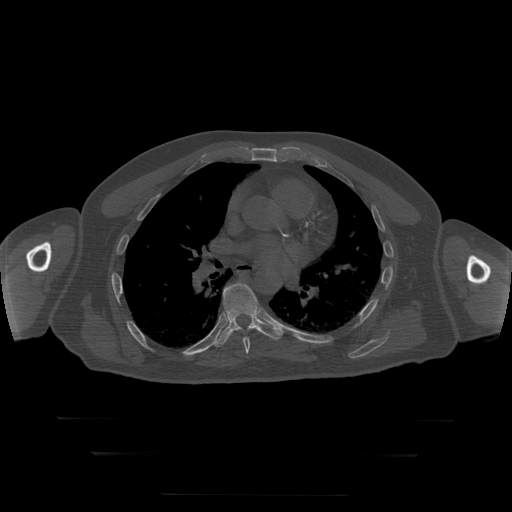
CT including the spine, one axial slice; slice 174 of 397 in the series (ordered by position); reconstruction kernel STANDARD; 120 kVp; bone window (W 1800 / L 400 HU); 1.25 mm slice thickness; 512 × 512 image matrix, field of view 510 × 510 mm. Patient age 73 years. Case-level facts recorded for this patient, not image findings: primary cancer: prostate.
Annotated regions visible in this slice (semi-automatically segmented with operator editing):
- T7 vertebra: bounding box (x1, y1, x2, y2) in pixels: (243, 338, 250, 354)
- T8 vertebra: (210, 283, 283, 348)